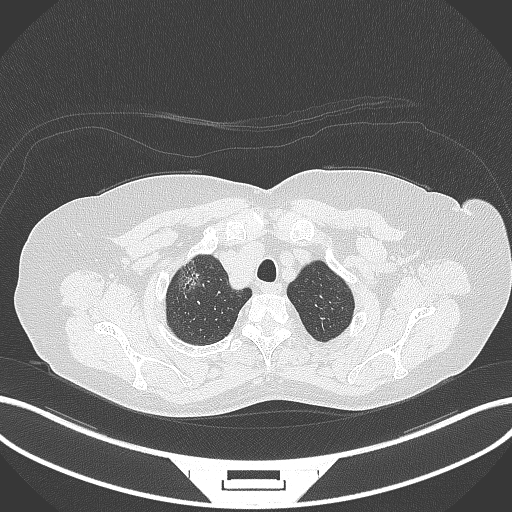
Chest CT, one axial slice. Position 311 of 365 along the scan axis. Reconstruction kernel B70f. Lung window (W 1500 / L -600 HU). 1 mm slice thickness. 512 × 512 image matrix, field of view 400 × 400 mm. Female patient, age 62 years. Case-level facts recorded for this patient, not image findings: clinical TNM (as recorded): T1c N0 M0.
Outlined on this slice (rectangle marked by the reading radiologist):
- lung tumour (recorded histology: adenocarcinoma): bounding box [x1, y1, x2, y2] px = [176, 261, 208, 296]